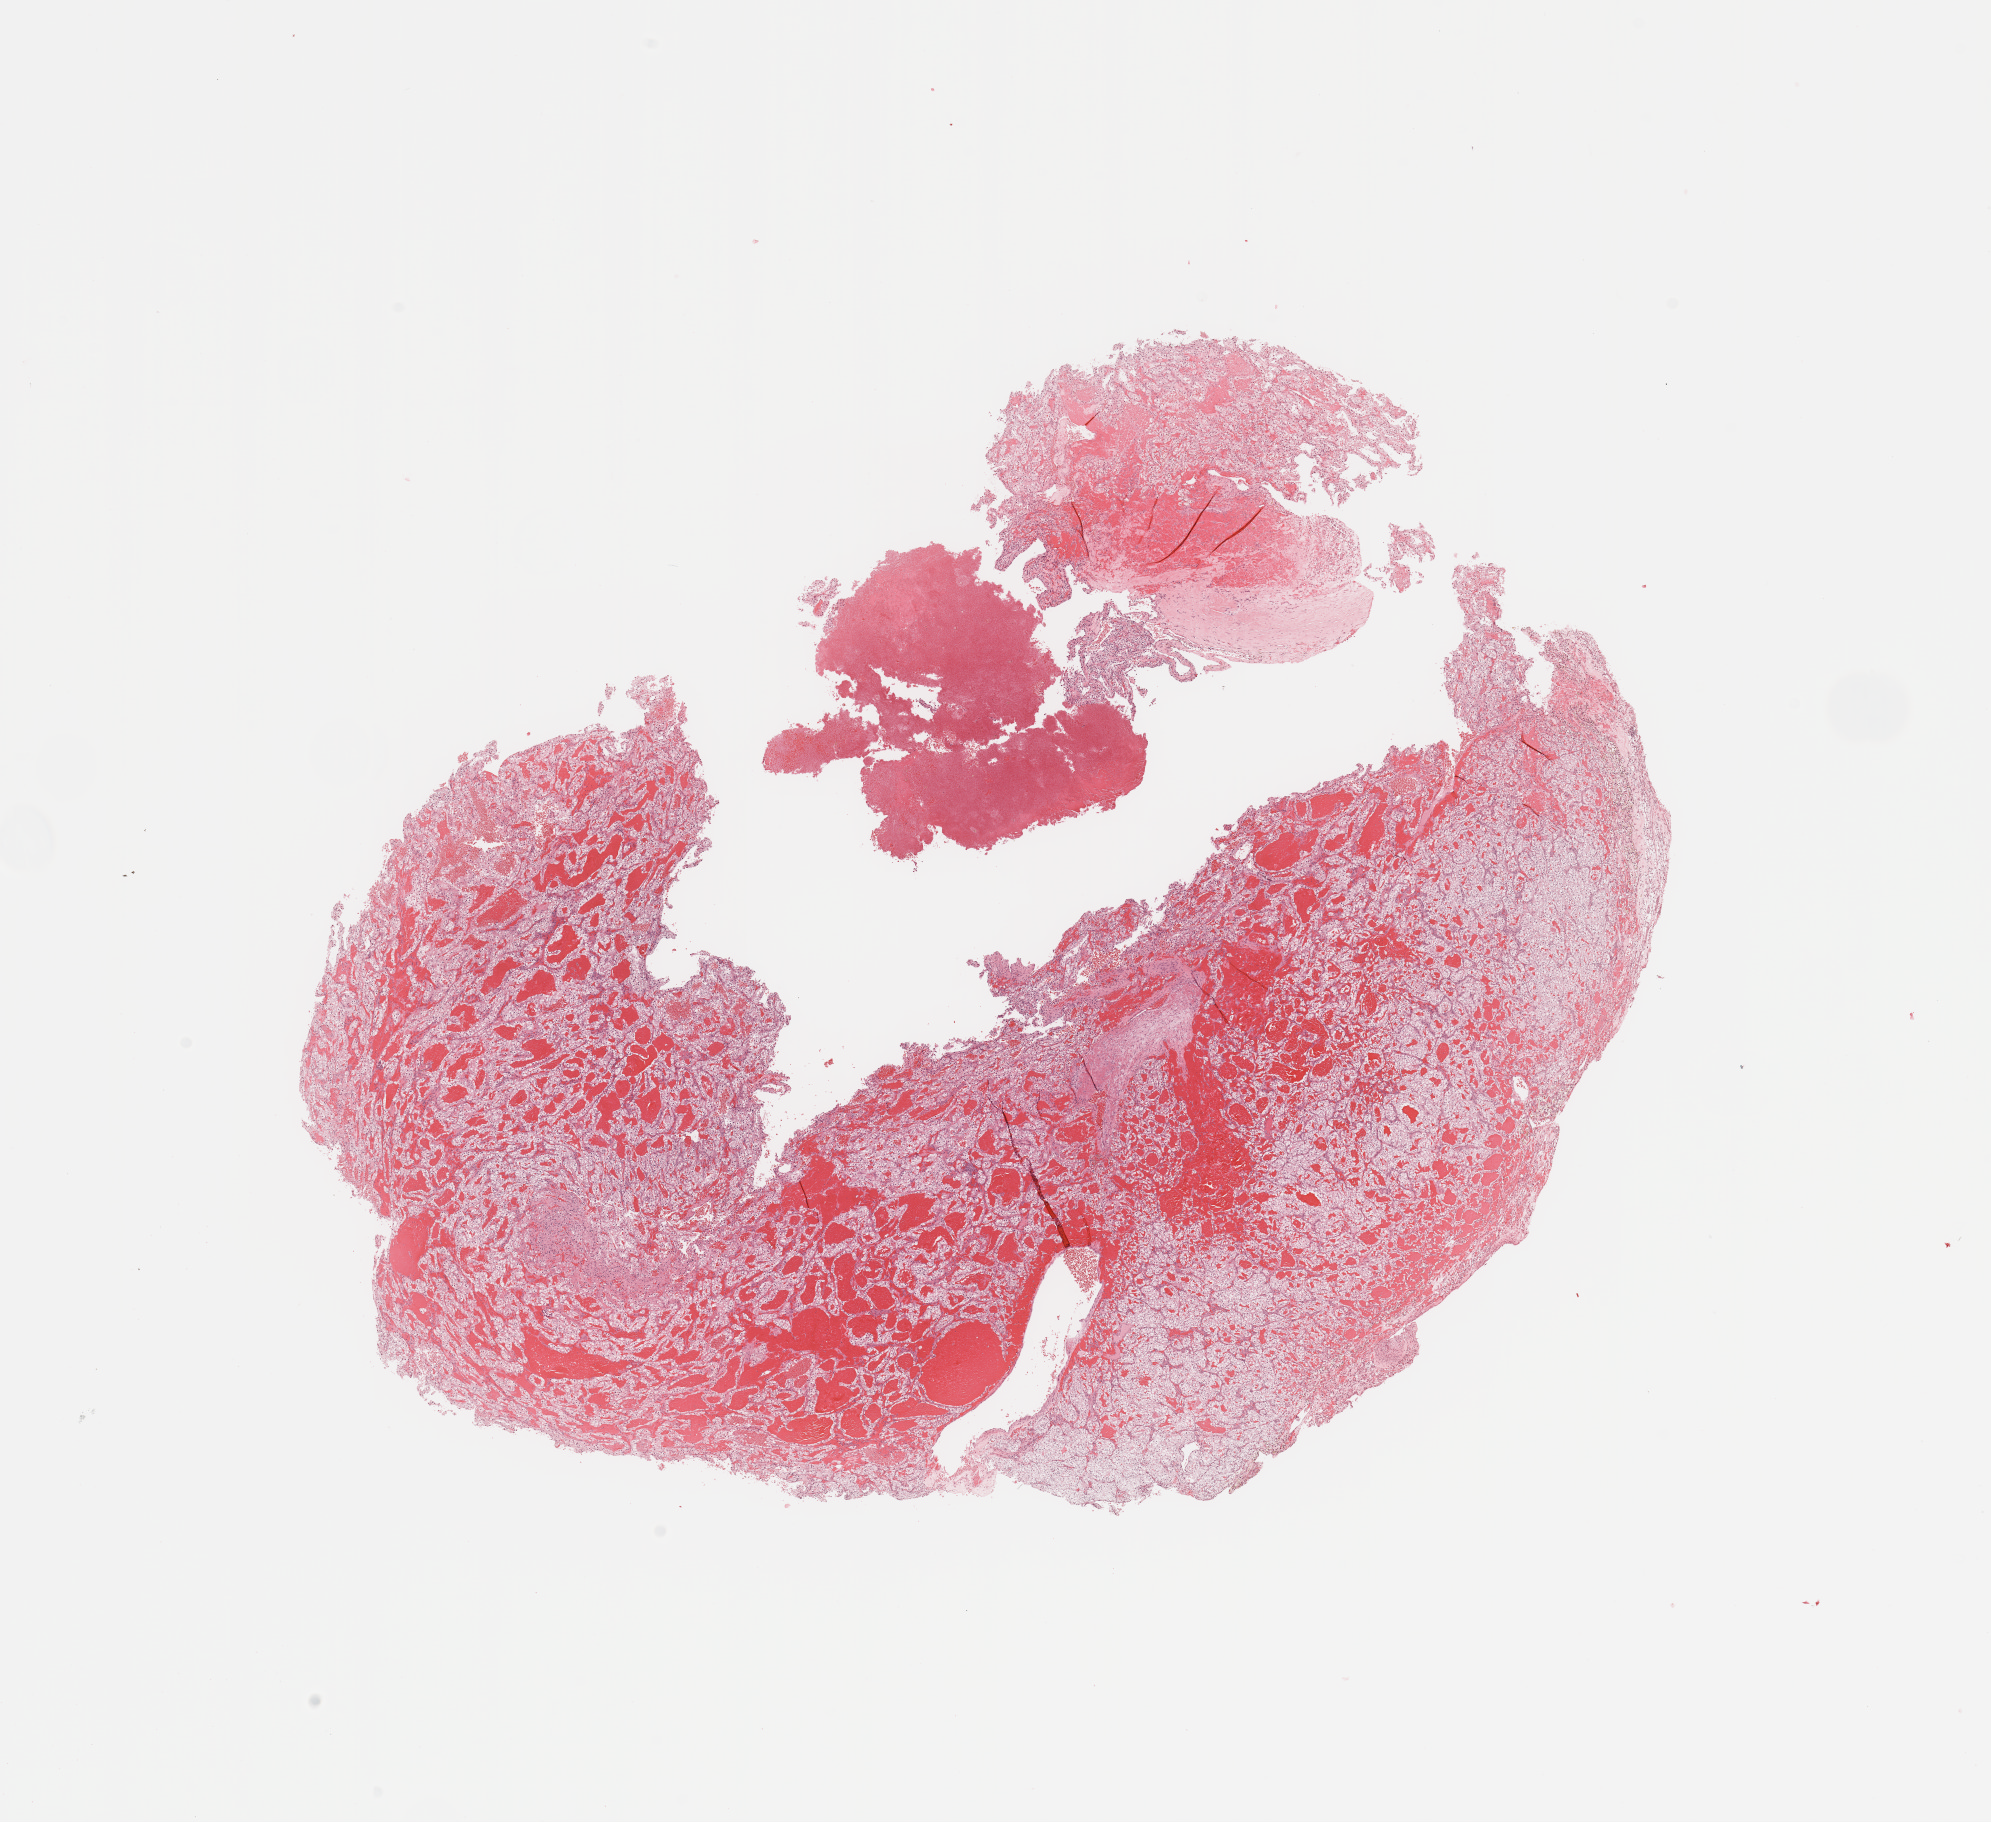
Digitized Hematoxylin and eosin (H&E) stained tissue section (whole slide) — whole scanned area (about 15.8 x 14.4 mm, slide scanned at 20x) shown as a low-resolution overview, tumour tissue sample, sampled site: kidney. Male, 68 y/o. Histologic grade: G2 (moderately differentiated). Slide review estimates, as recorded: tumour nuclei 80%, necrosis 2%.
Primary tumour site (as recorded): upper pole. AJCC pathologic stage: I. Diagnosis: Renal cell carcinoma, NOS.